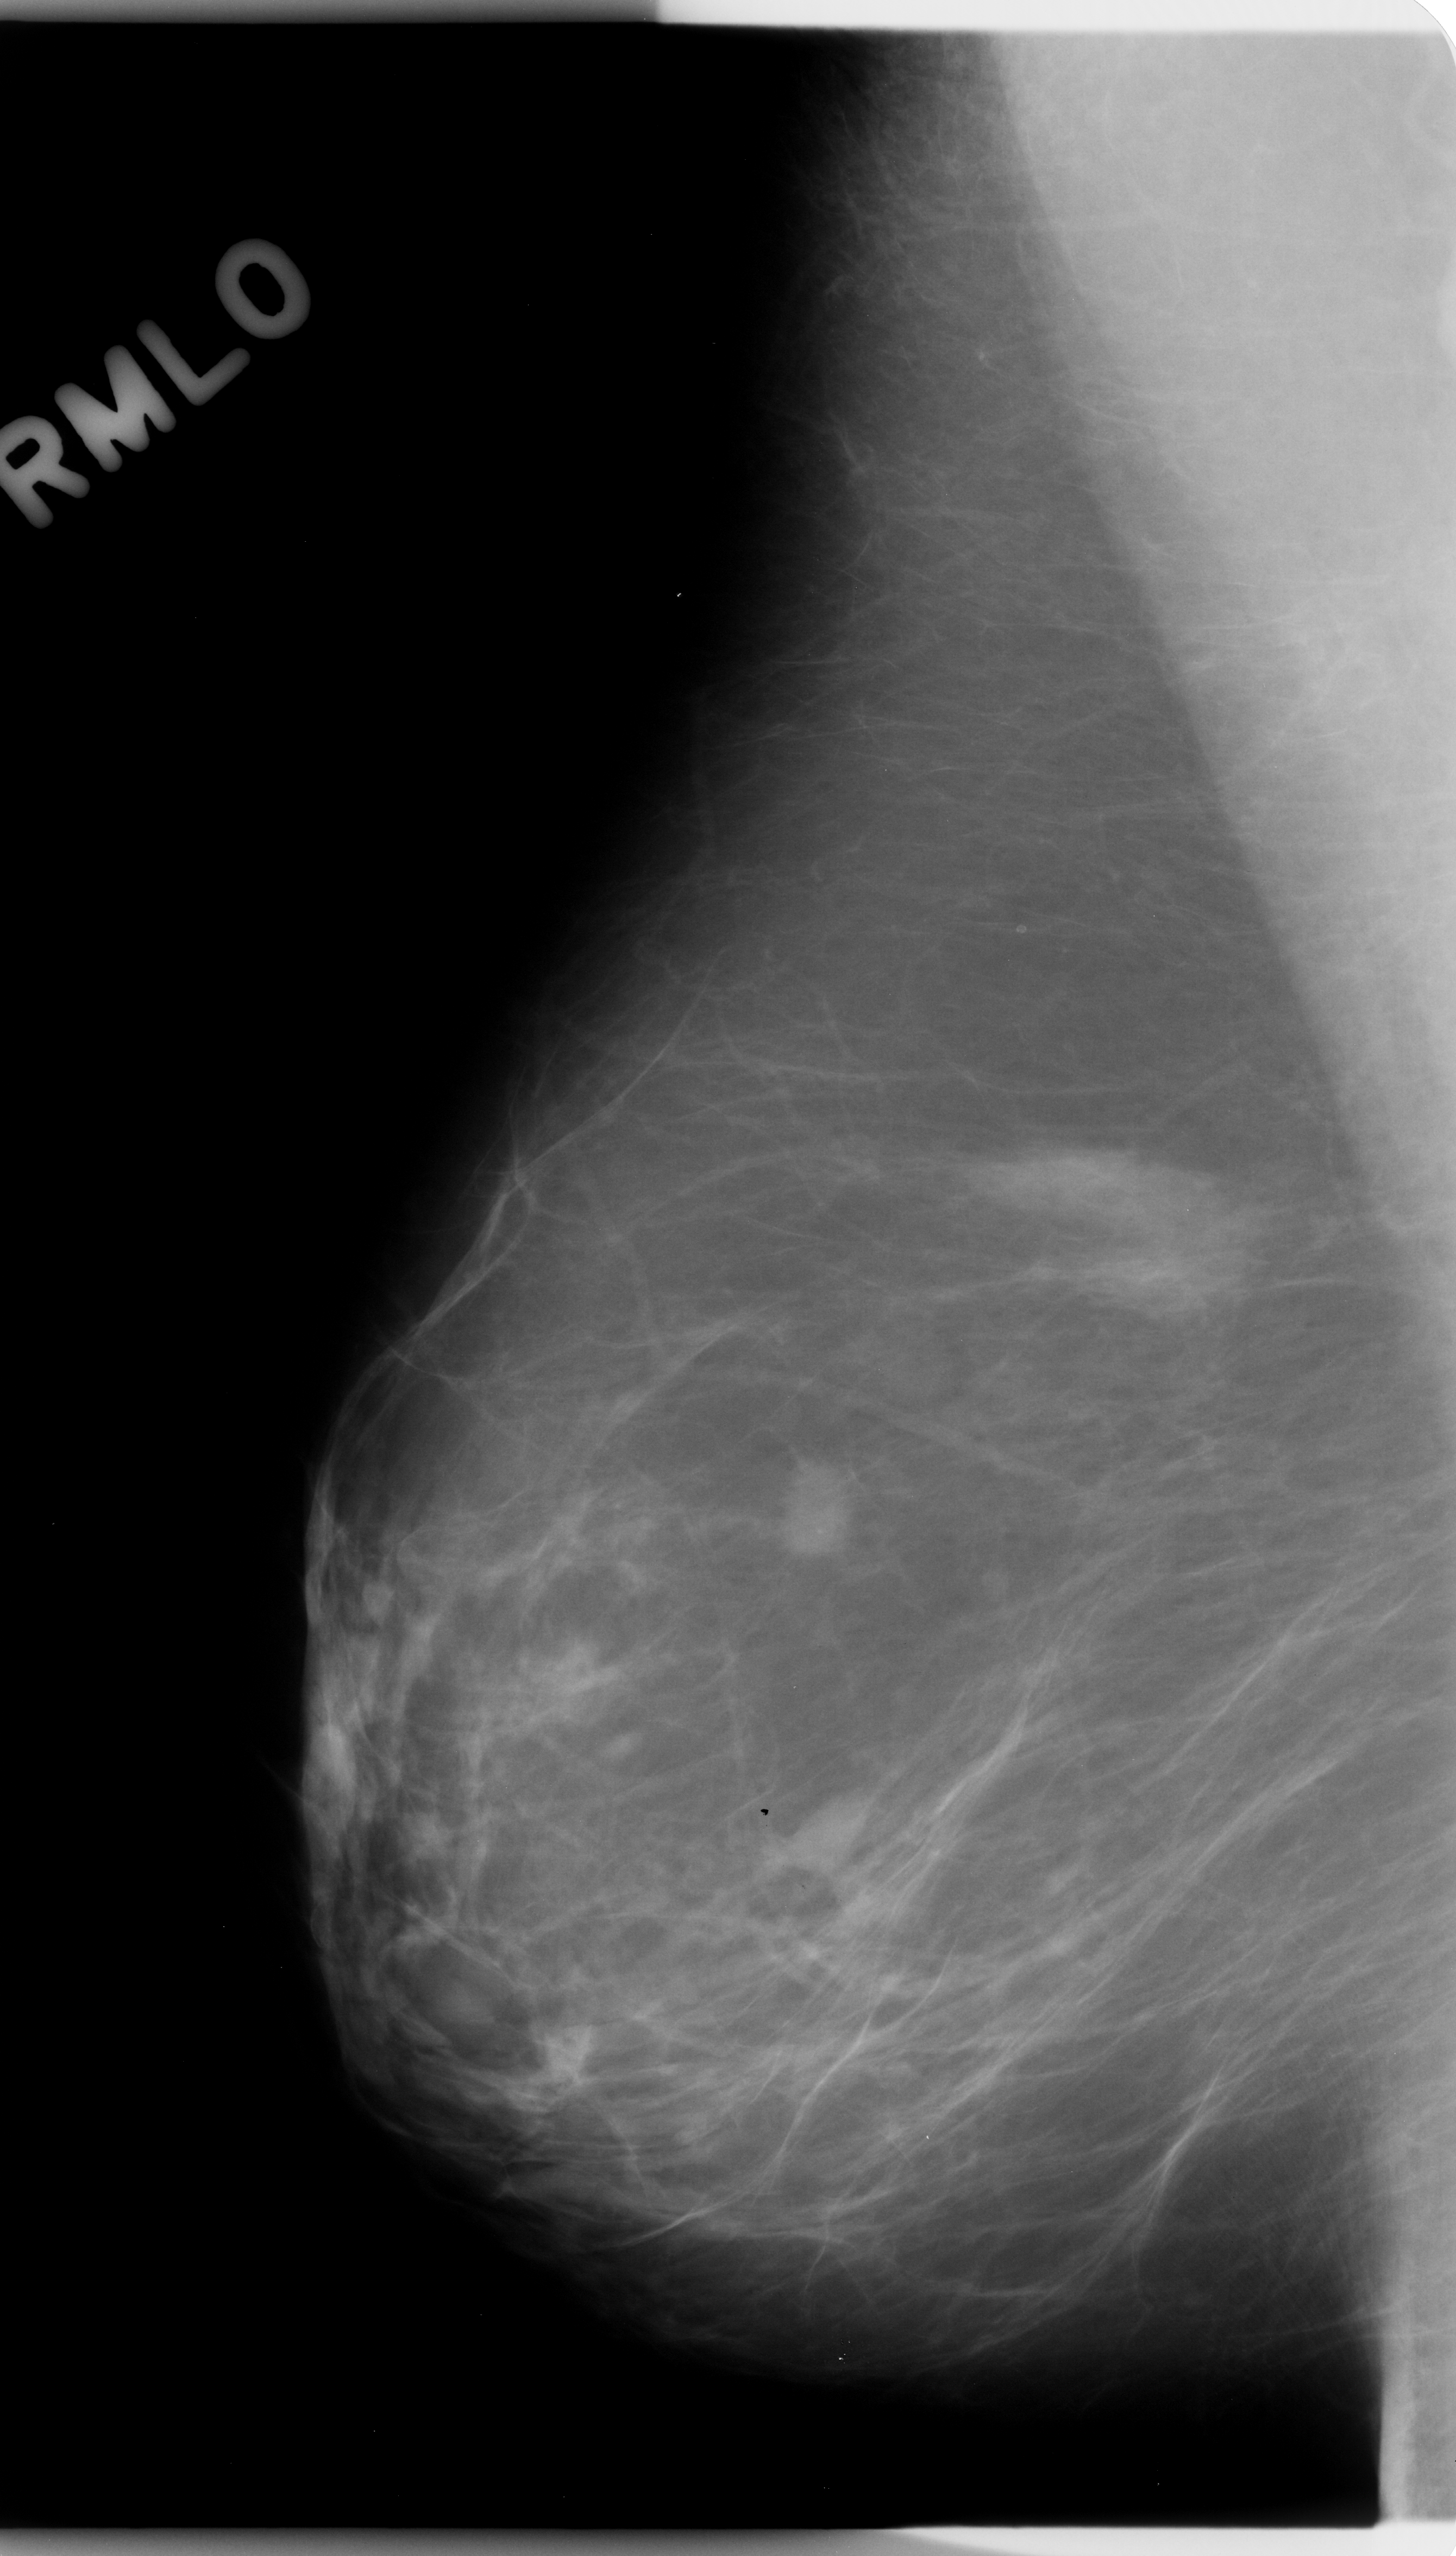
Digitized screen-film mammogram, right breast, mediolateral oblique (MLO) view, BI-RADS breast density category 1 (scale 1–4).
Marked abnormality: mass, shape oval, margins spiculated; BI-RADS assessment category 5; subtlety rating 5 on a 1 (subtle) to 5 (obvious) scale; pathology result (as recorded, not read from the image): malignant.